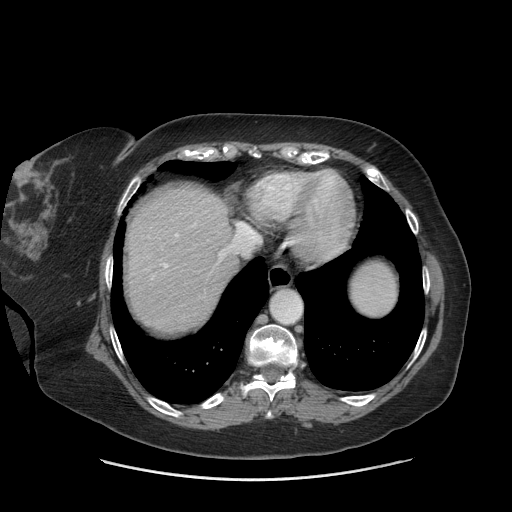
Contrast-enhanced abdominal CT (liver protocol), one axial slice. Position 63 of 69 along the scan axis. Reconstruction kernel STANDARD. 140 kVp. Soft-tissue window (W 400 / L 40 HU). 512 × 512 image matrix, field of view 420 × 420 mm. Case-level facts recorded for this patient, not image findings: diagnosis: hepatocellular carcinoma (patient treated with transarterial chemoembolisation; whether this scan precedes or follows treatment is not stated here); TNM stage (as recorded): Stage-IIIB; Child-Pugh class: A; tumour differentiation: moderately differentiated; tumour nodularity: multinodular.
Annotated regions visible in this slice (semi-automatic segmentation, software-assisted and operator-edited):
- abdominal aorta: bounding box <271,291,301,323> (left, top, right, bottom; pixels)
- liver parenchyma outside the tumour (the mass and vessels are separate outlines, so this box may not span the whole liver): <126,186,238,332>
- liver vessels: <163,234,225,268>